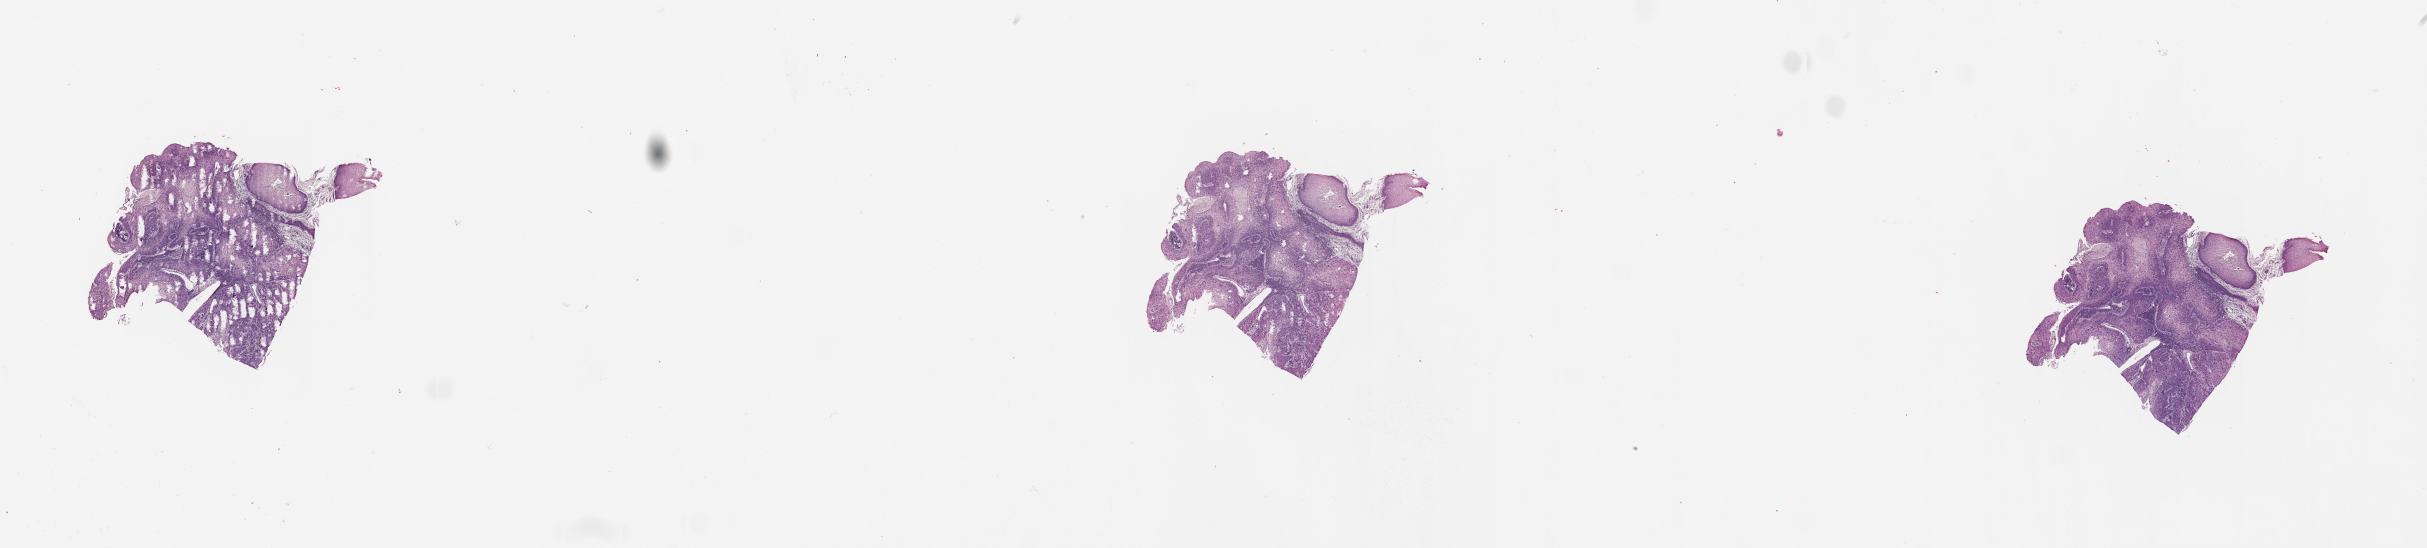
H&E whole-slide image, shown as a low-resolution overview of the whole scanned area (about 39.1 x 8.8 mm, slide scanned at 20x), tumour tissue sample, sampled site: tongue. Male, 76 y/o. Histologic grade: G2 (moderately differentiated). Slide review estimates, as recorded: tumour nuclei 85%, necrosis 5%.
• AJCC pathologic stage: II
• histologic diagnosis: Squamous cell carcinoma, NOS (tongue, NOS)
• primary tumour site (as recorded): oral cavity